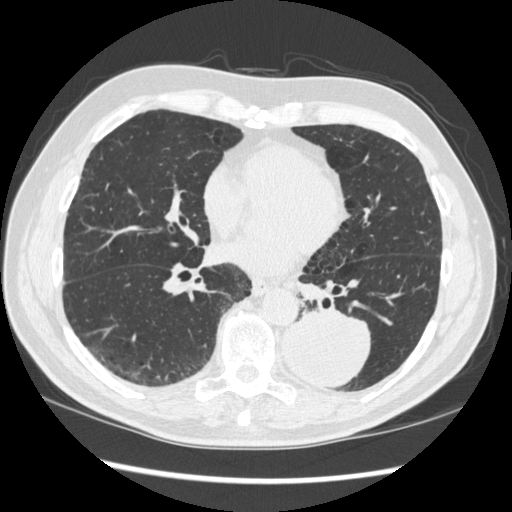
Low-dose screening chest CT, one axial slice; slice 141 of 348 in the series (ordered by position); lung window (W 1500 / L -600 HU); 1.25 mm slice thickness; 512 × 512 image matrix, field of view 360 × 360 mm.
Outlined on this slice (outlined manually by an expert reader):
- lesion 1 (tumor, lower lobe of left lung): bounding box [x1, y1, x2, y2] px = [283, 310, 372, 388]